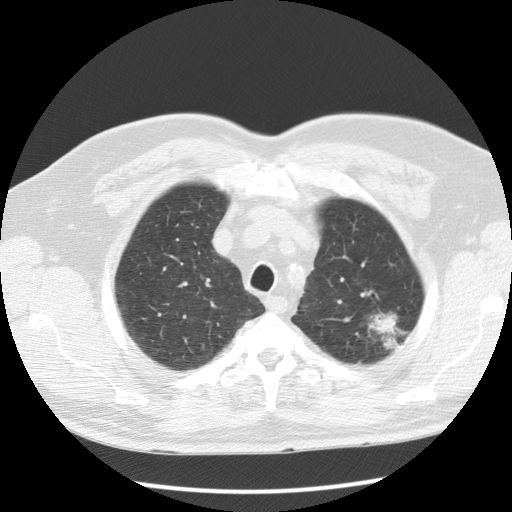
Low-dose screening chest CT, axial slice, baseline annual screen, lung window (W 1500 / L -600 HU). Male participant, aged 60 years at enrolment.
Lesion marked by an expert reader, bounding box <355,297,415,358> (left, top, right, bottom; pixels). The screening reader recorded 3 non-calcified nodules or masses ≥4 mm on this exam (left upper lobe, right upper lobe, left upper lobe); which of them this box marks is not recorded. Official screen result: positive, change unspecified: nodule(s) >= 4 mm or enlarging nodule(s), mass(es), or other non-specific abnormalities suspicious for lung cancer. Participant outcome: lung cancer diagnosed 48 days after this screen — bronchiolo-alveolar adenocarcinoma, NOS, left upper lobe, well differentiated (G1), stage IA (AJCC 6th edition), 27 mm at pathology.